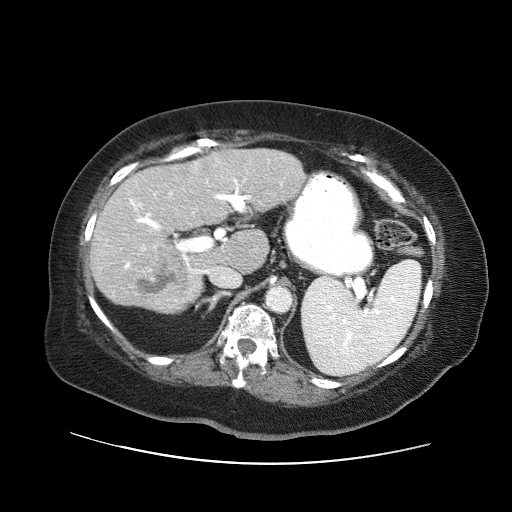
Contrast-enhanced abdominal CT (liver protocol), one axial slice. Slice 31 of 71 in the series (ordered by position). Reconstruction kernel STANDARD. 120 kVp. Soft-tissue window (W 400 / L 40 HU). 2.5 mm slice thickness. 512 × 512 image matrix. From the clinical record (not read from this slice): diagnosis: hepatocellular carcinoma (patient treated with transarterial chemoembolisation; whether this scan precedes or follows treatment is not stated here); TNM stage (as recorded): Stage-II.
Annotated regions visible in this slice (semi-automatic segmentation, software-assisted and operator-edited):
- liver parenchyma outside the tumour (the mass and vessels are separate outlines, so this box may not span the whole liver): bounding box [x1, y1, x2, y2] px = [90, 148, 304, 312]
- mass: [133, 245, 189, 297]
- liver vessels: [124, 162, 282, 301]